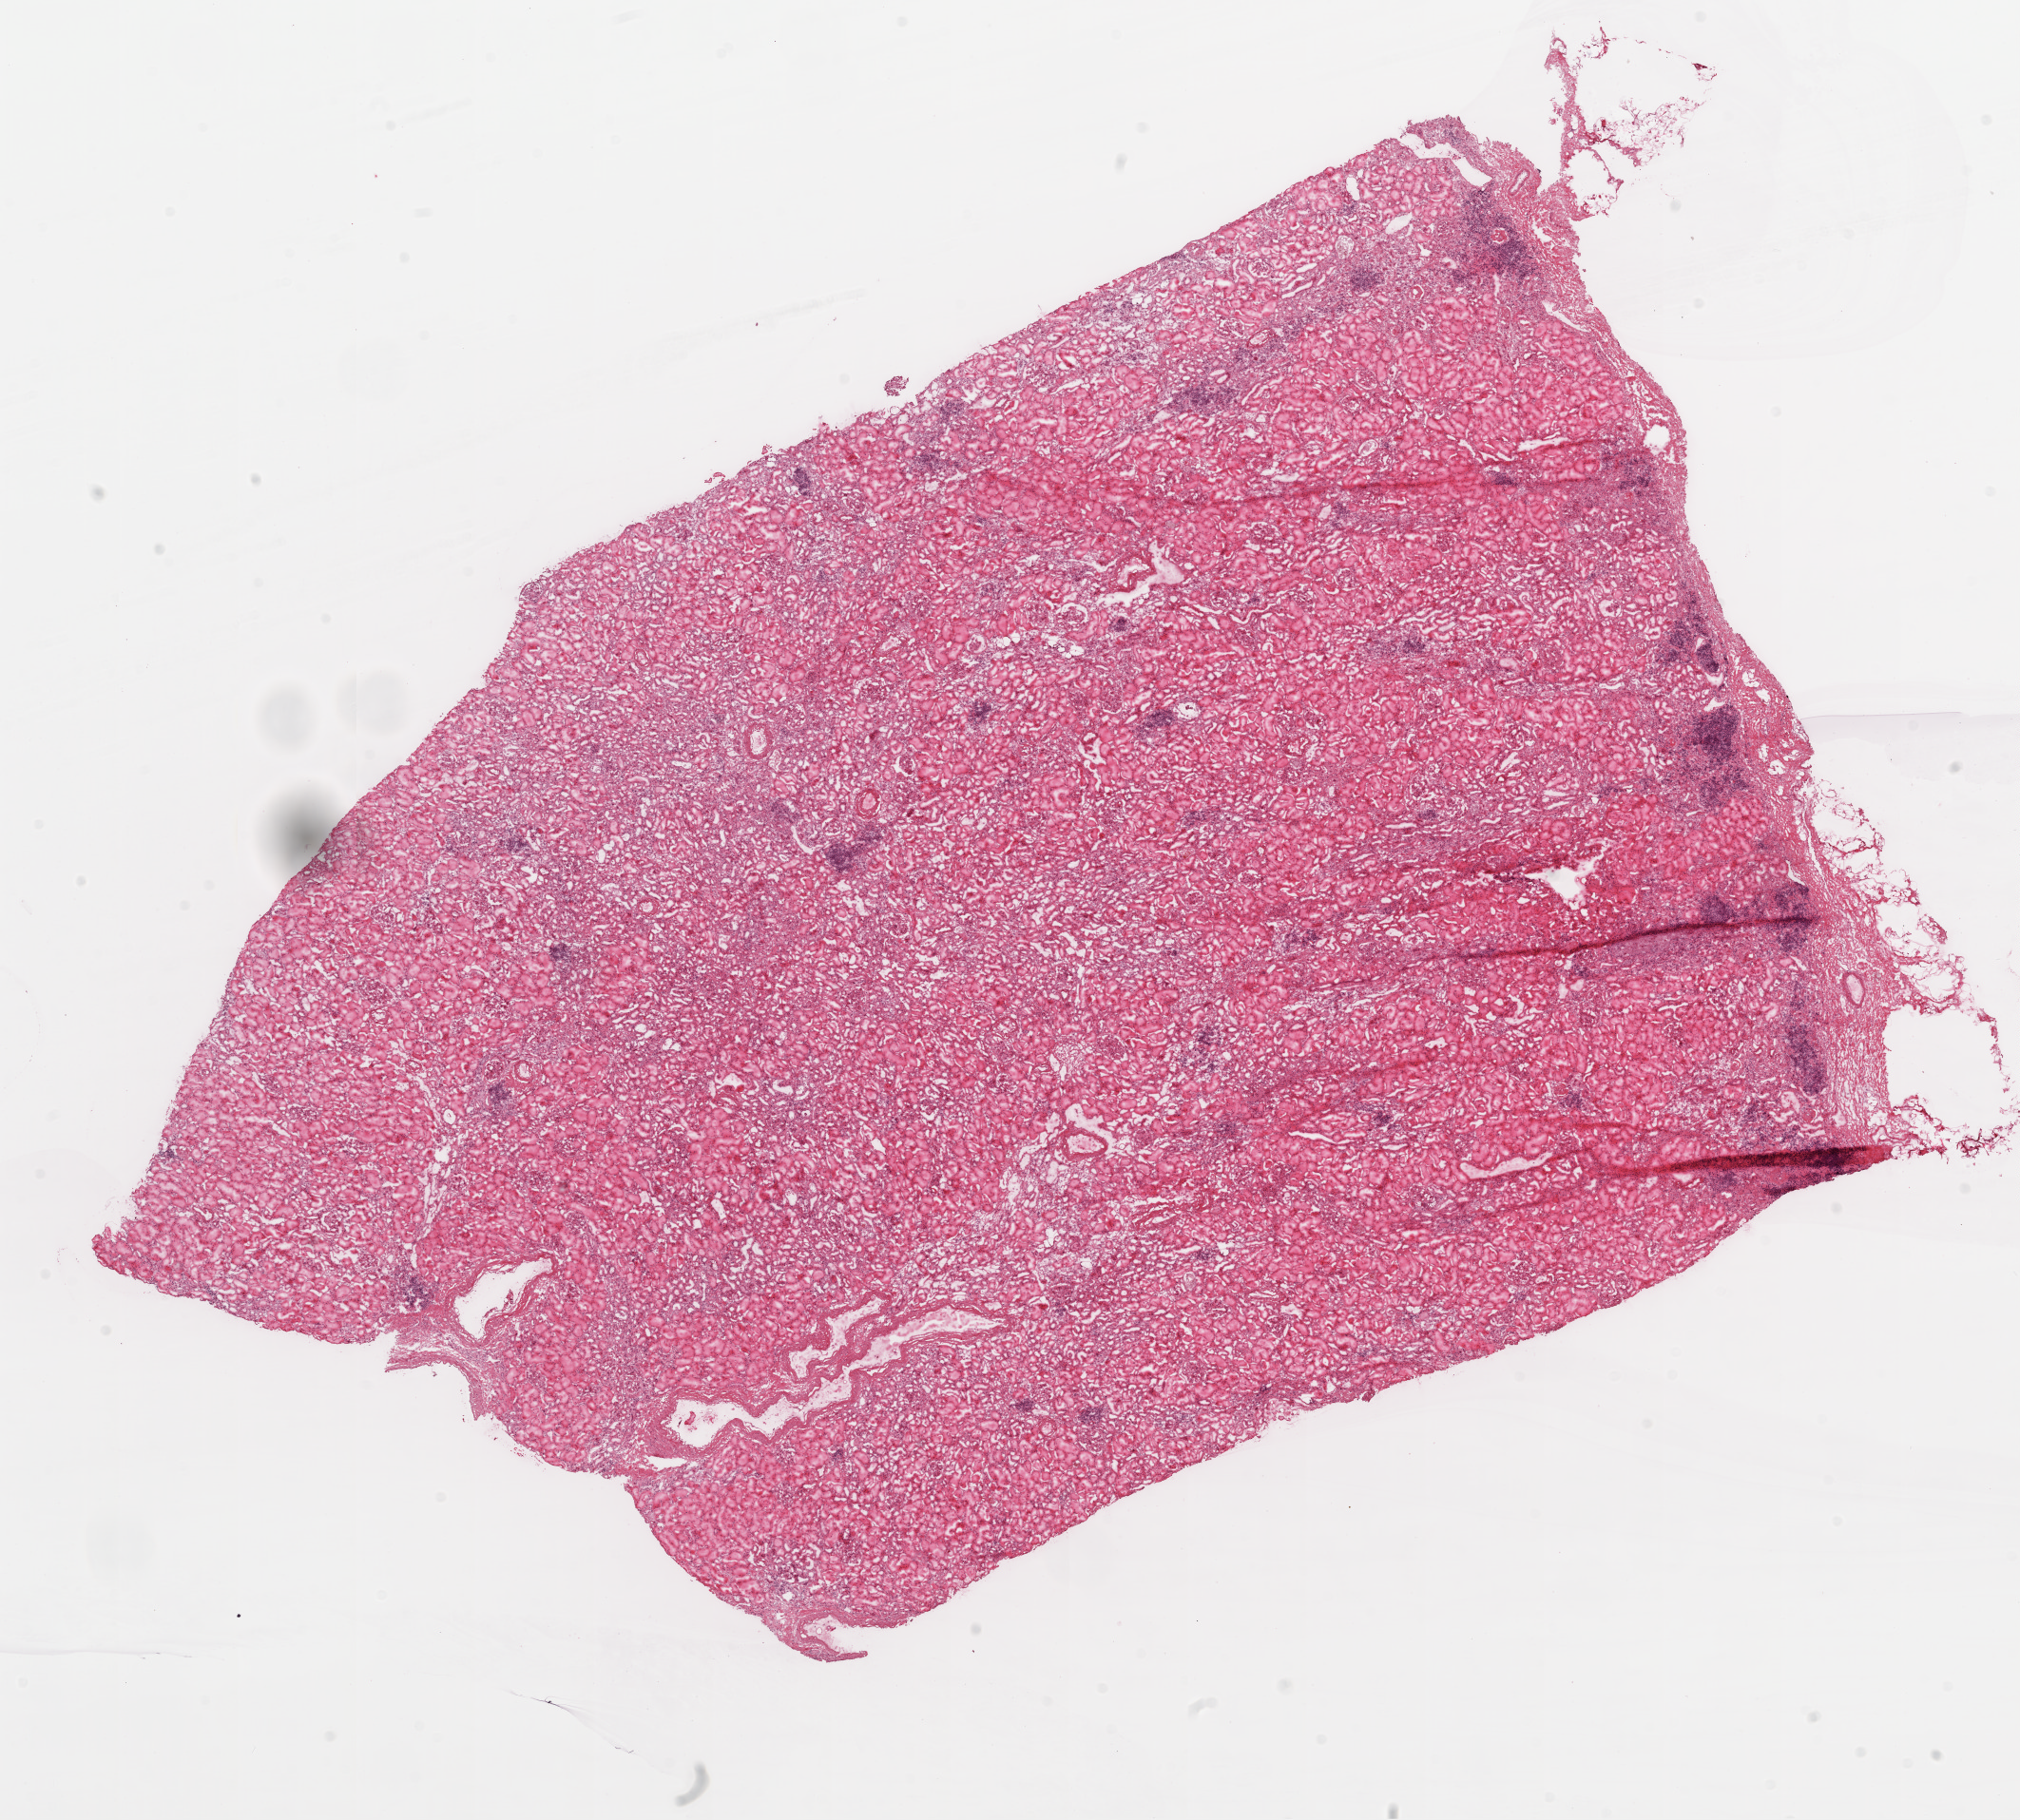
Digitized H&E-stained tissue section (whole slide), shown as a low-resolution overview of the whole scanned area (about 17.1 x 15.4 mm, from a 20x scan). Frozen section from the top of the tissue portion. Kidney, solid tissue normal (non-tumour tissue) sample. Male patient; age at initial diagnosis 70 years.
This section: solid tissue normal (non-tumour) sample from the same patient. Patient diagnosis: Clear cell adenocarcinoma, NOS.